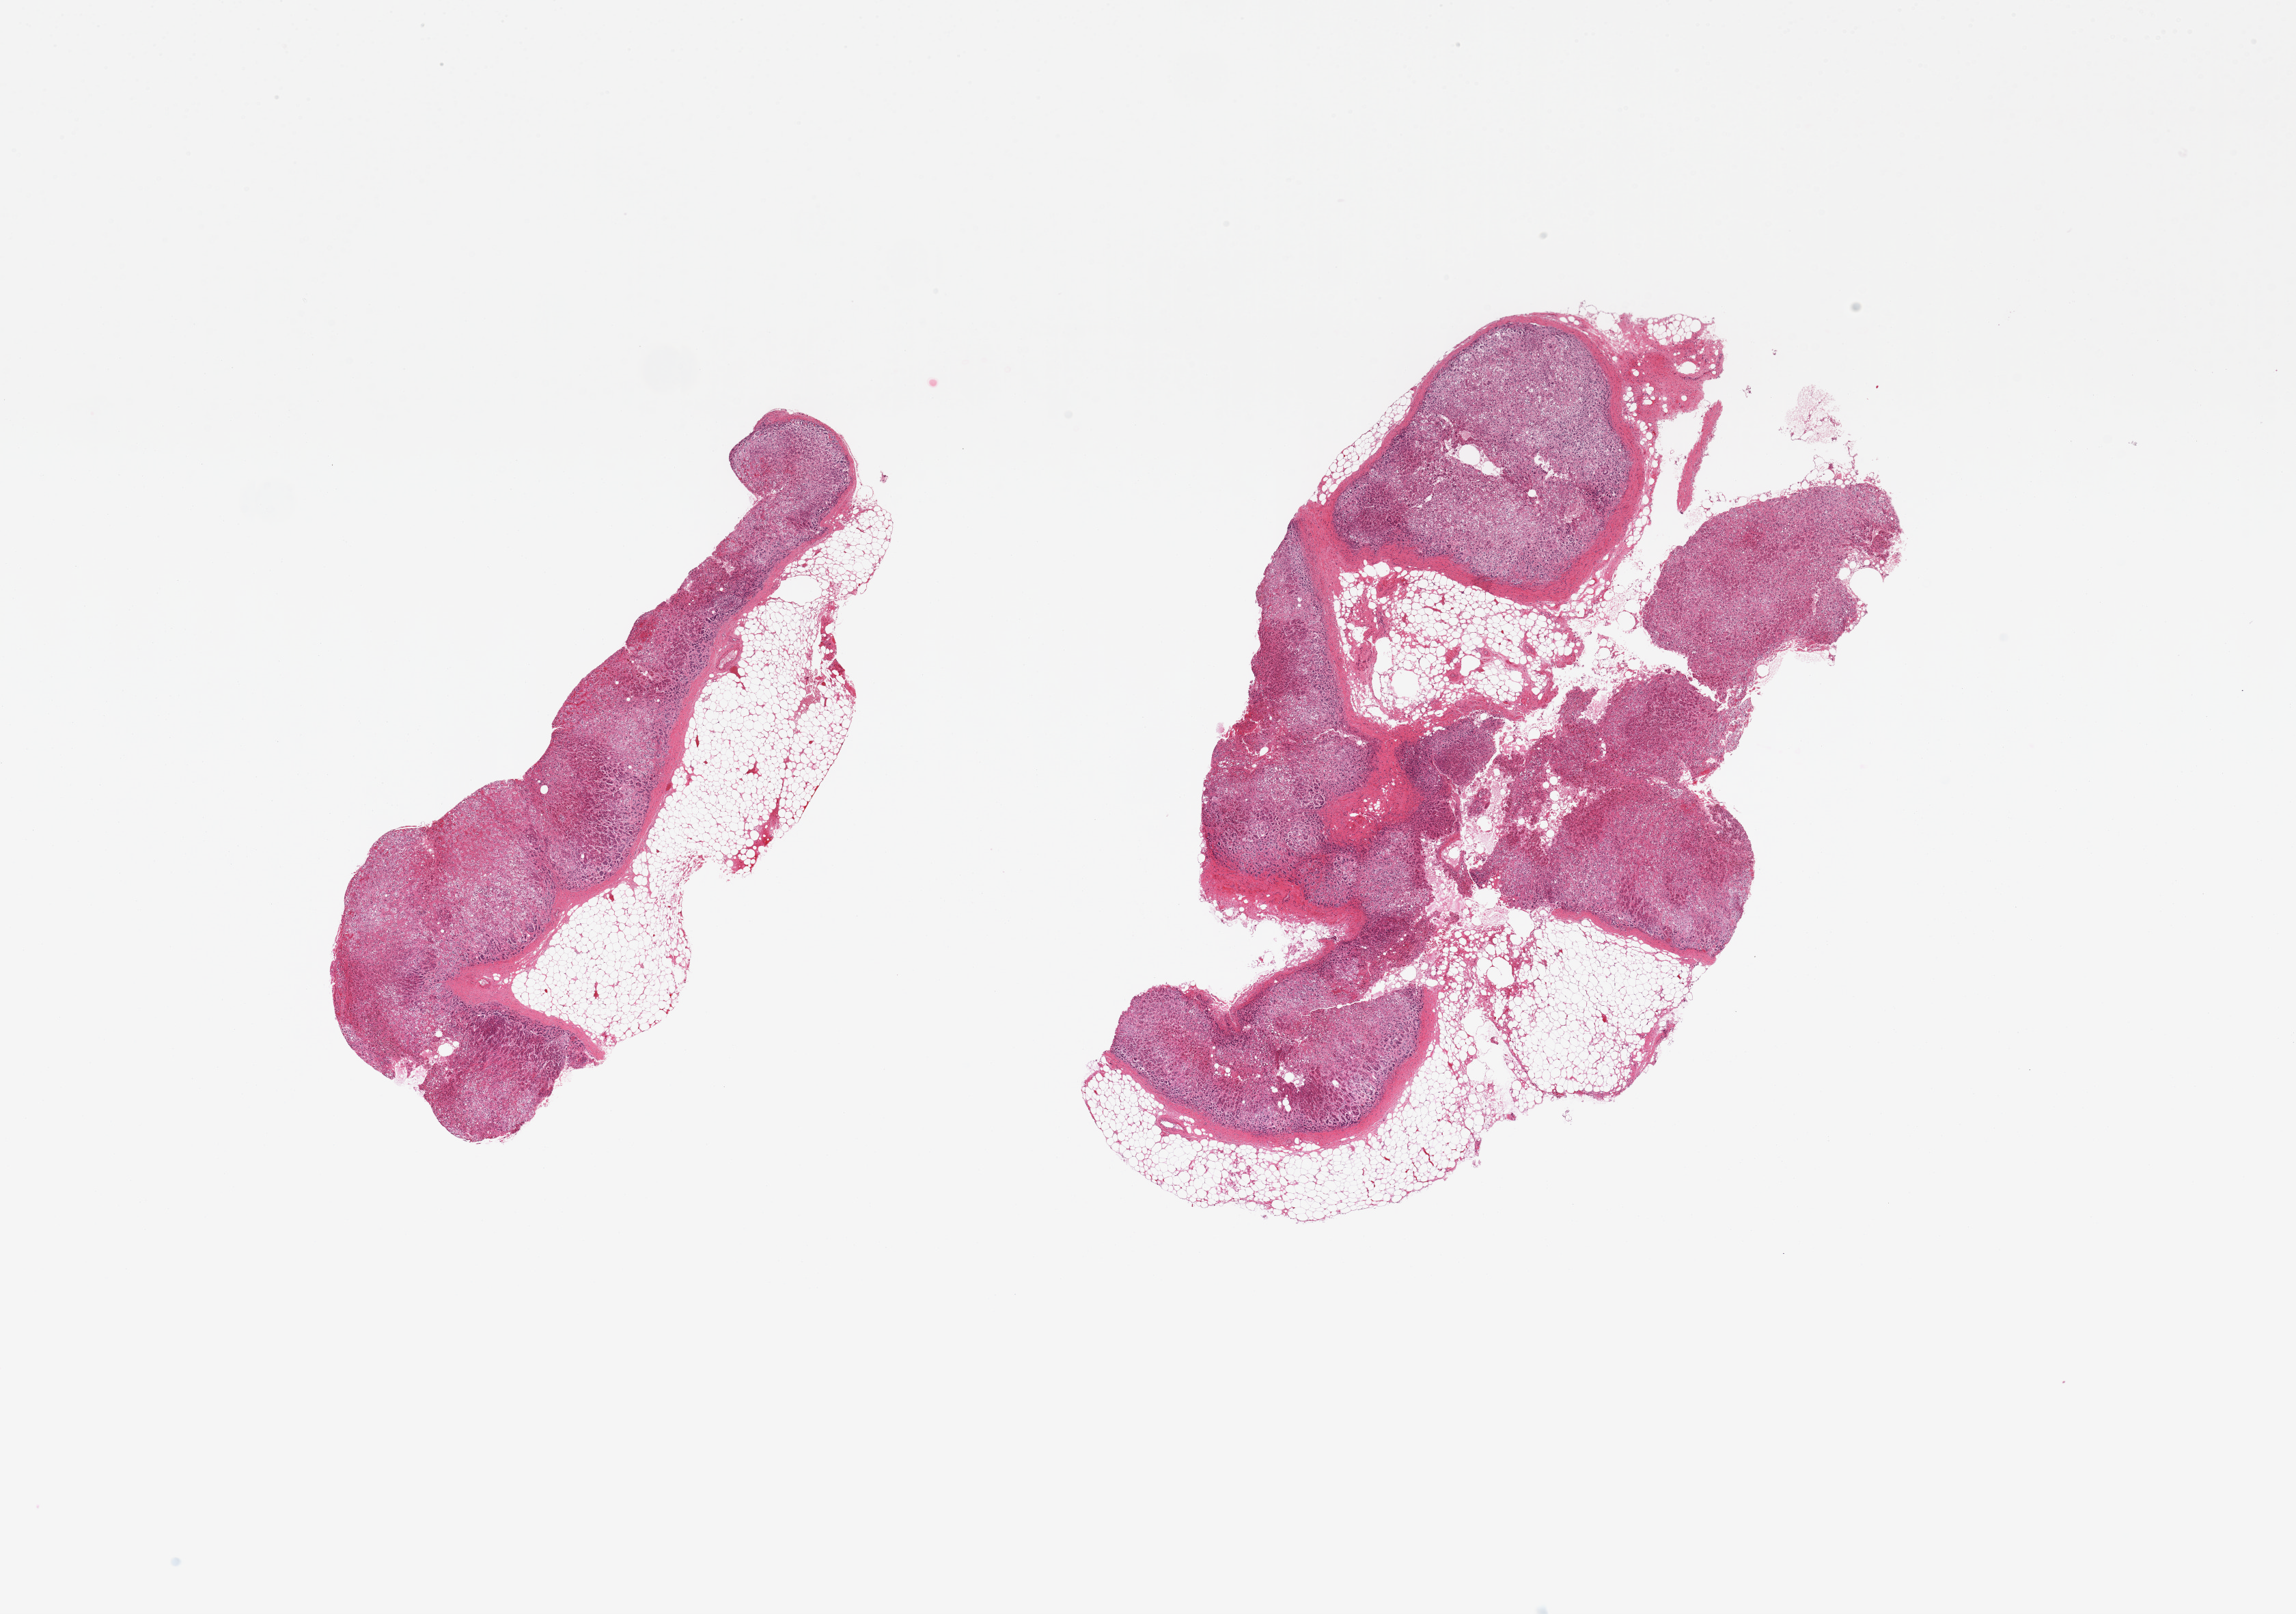
Digitized haematoxylin and eosin-stained section, shown as a low-resolution overview of the whole scanned area (about 26.6 x 18.7 mm, slide scanned at 20x), PAXgene-fixed paraffin-embedded (PFPE) section, target tissue: adrenal gland, tissue donor sample. Donor: male.
Review note (as recorded): 2 pieces, cortex, advanced autolysis, ~30-40% adherent/interstitial fat.